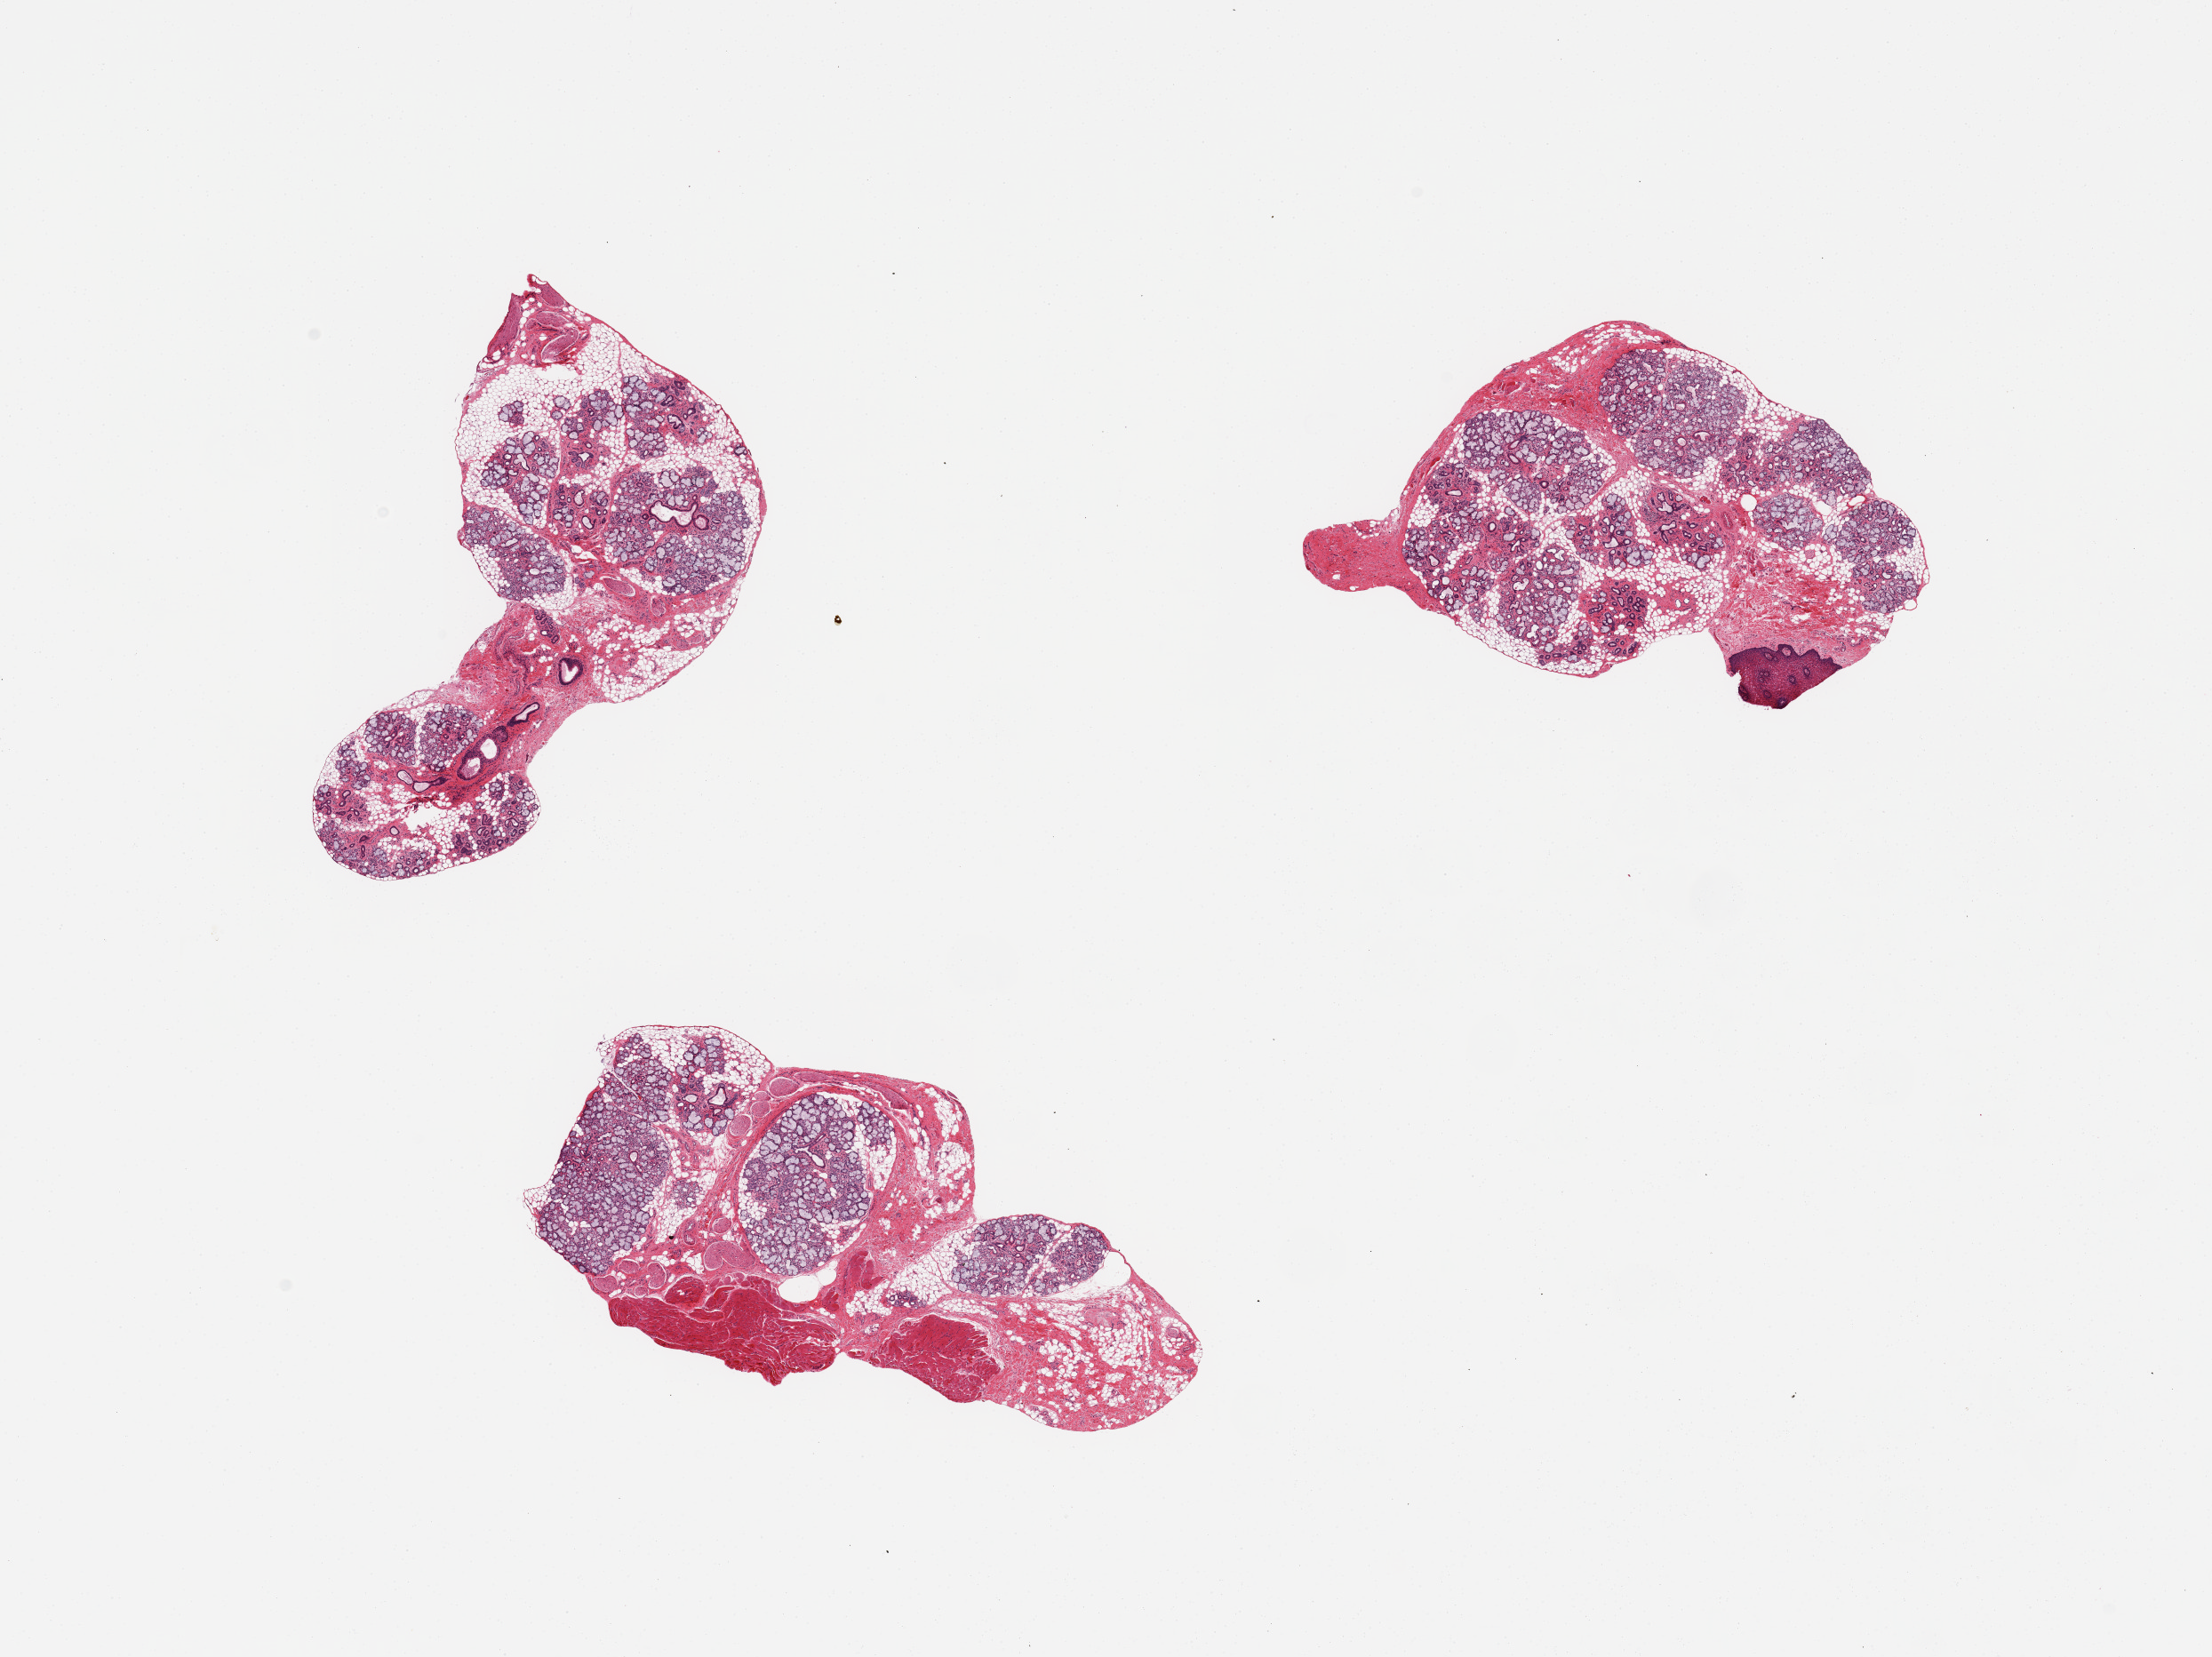
Digitized hematoxylin and eosin (H&E)-stained section — low-resolution overview of the scanned area, about 19.7 x 14.8 mm (from a 20x scan), PAXgene-fixed, paraffin-embedded tissue, section of minor salivary gland (target tissue), donor tissue sample. Donor: male.
* pathologist's review note for this sample: 3 pieces; small amount of adherent skin and muscle, otherwise good glandular components